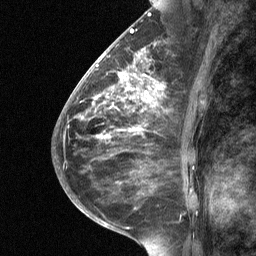
Breast MRI (dynamic contrast-enhanced), one sagittal slice; position 33 of 64 along the scan axis; dynamic contrast-enhanced study with each time point stored as its own series, time point 2 of 3 at this slice position (early post-contrast, ordered by acquisition time); 1.5 T; TE 4.8 ms, TR 27 ms; 2 mm slice thickness; 256 × 256 image matrix, field of view 180 × 180 mm. Female patient, age 59 years. From the clinical record (not read from this slice): setting: breast cancer imaged before/during neoadjuvant chemotherapy; receptor status: triple-negative.
Outlined on this slice (semi-automatic segmentation, software-assisted and operator-edited):
- analysis volume of interest (the breast-tissue region the enhancement analysis was run in; not a lesion): box from (x=113, y=66) to (x=160, y=118) px
- tumour enhancement mask (voxels above the 90 % enhancement threshold inside the analysis volume of interest): (x=119, y=72)–(x=156, y=102)